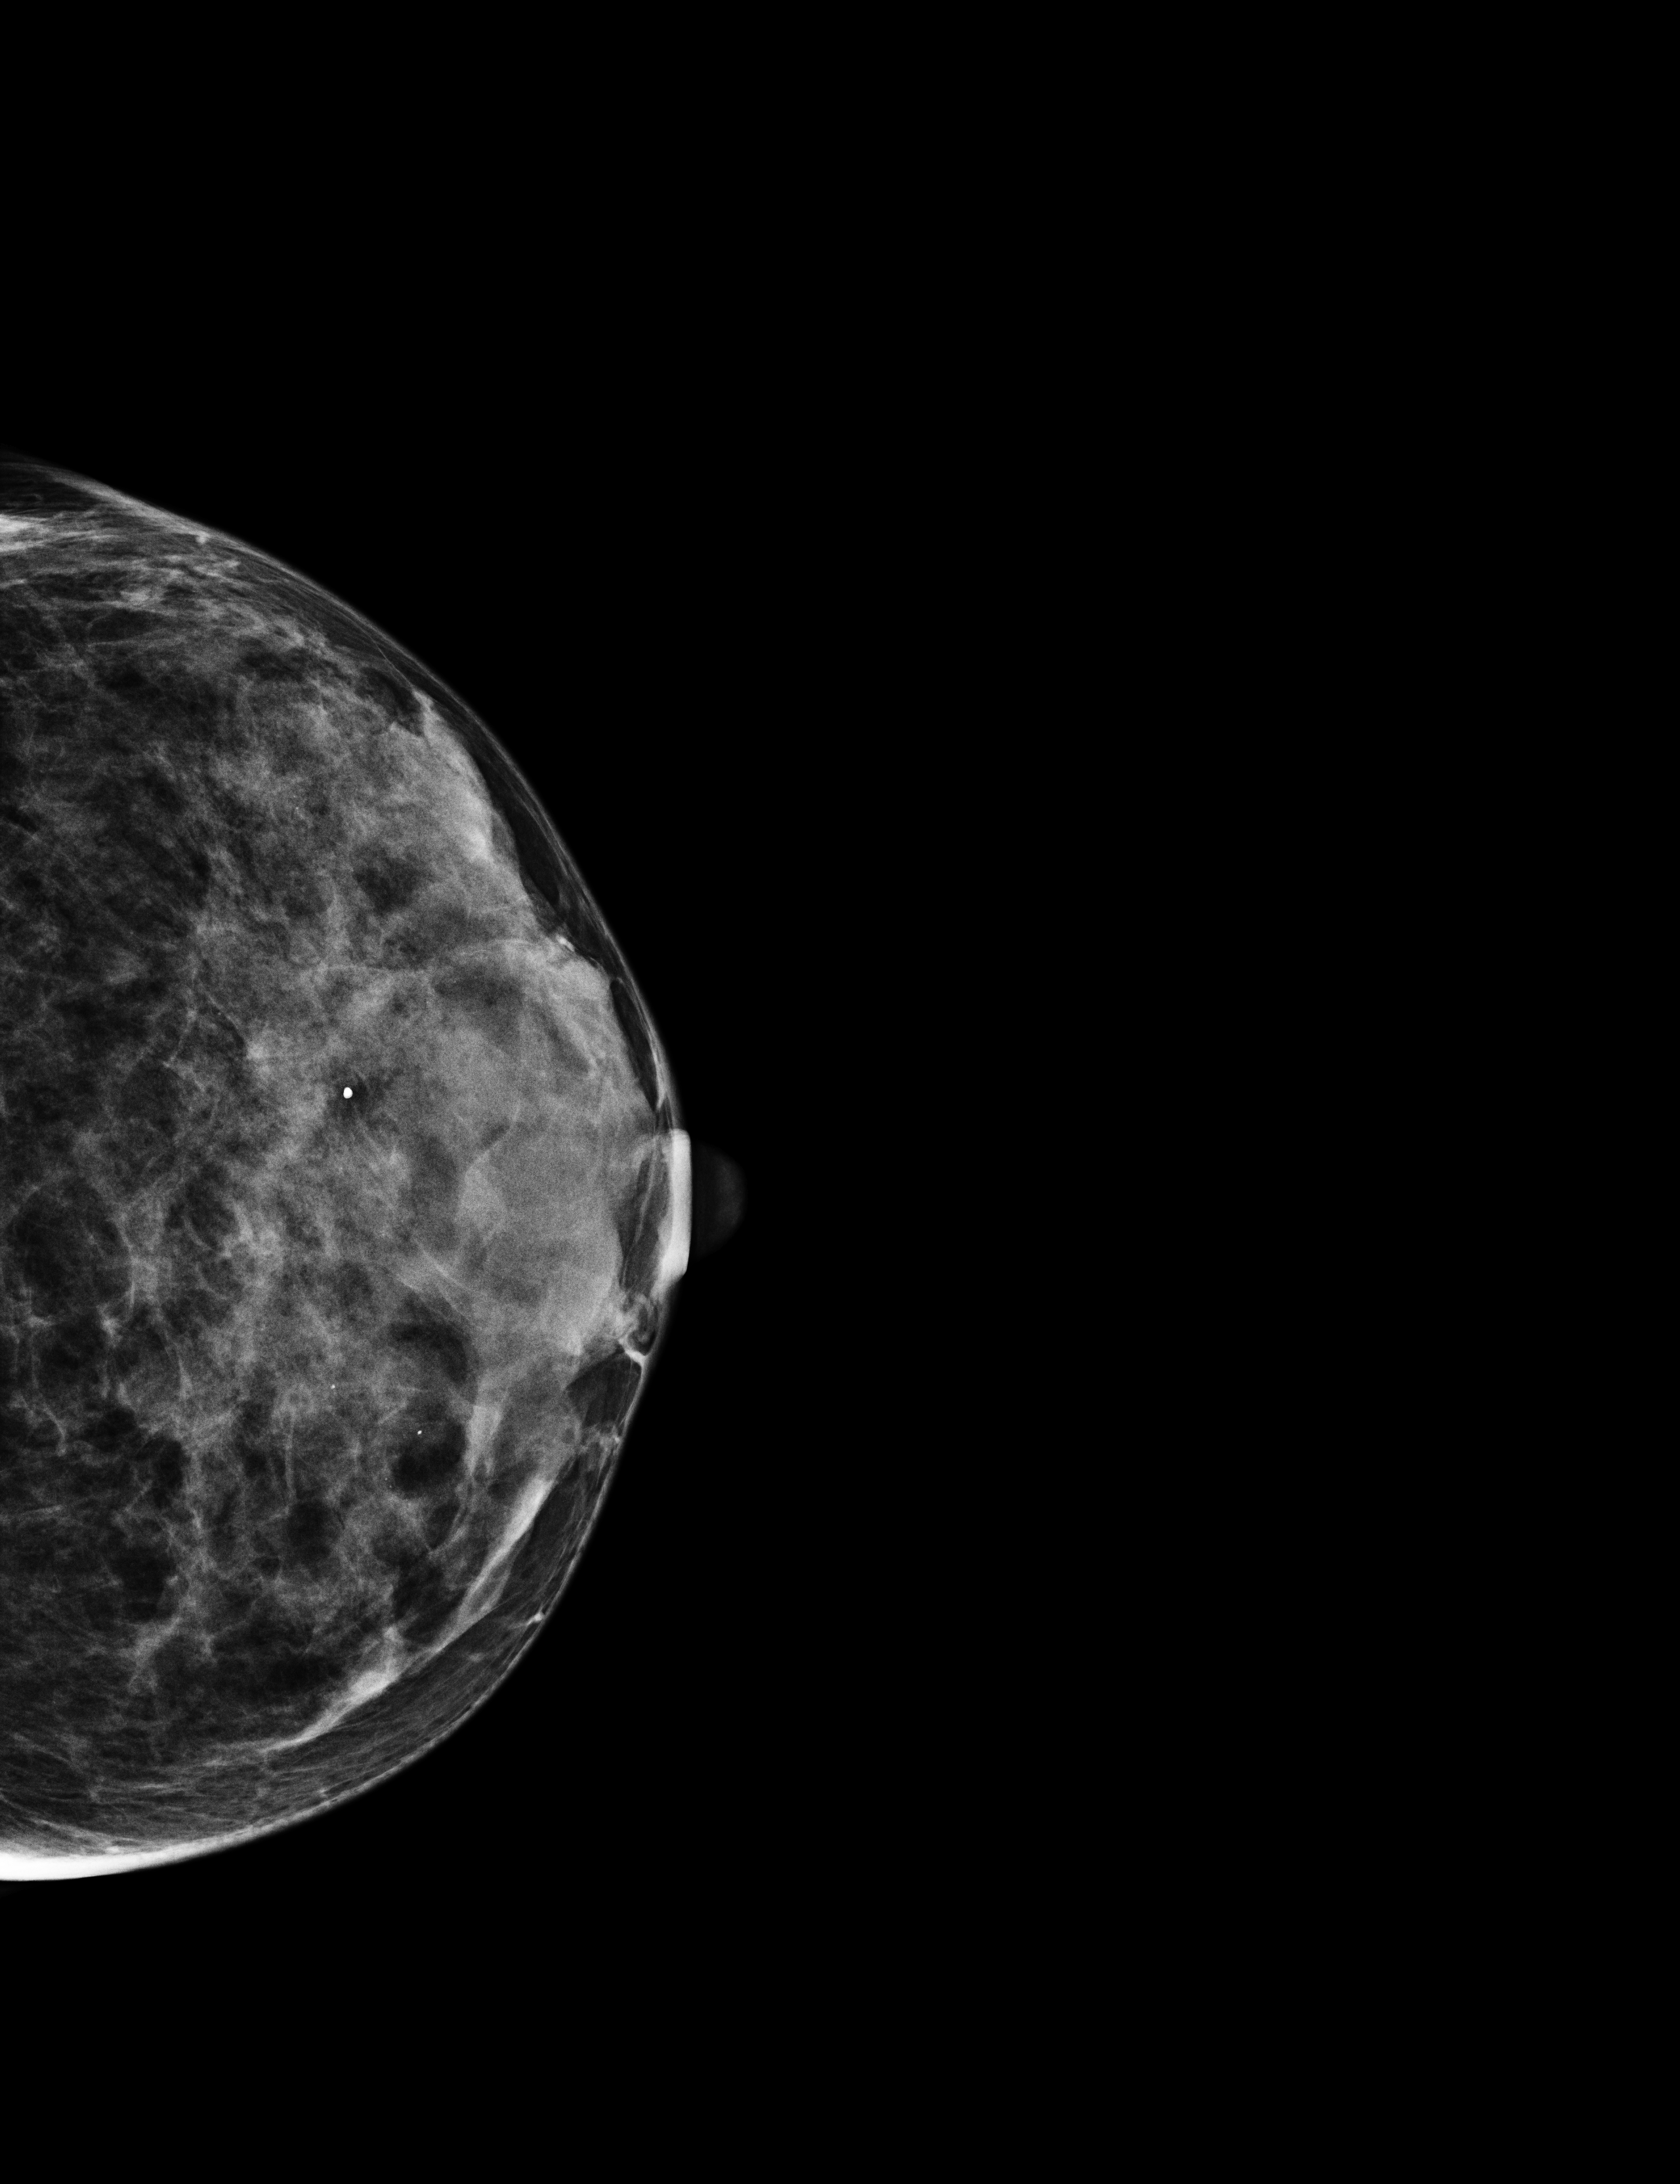
Screening examination; system: Selenia Dimensions. Female patient, age 59 years.
Image type: full-field digital mammogram. Breast: left. Projection: CC view.